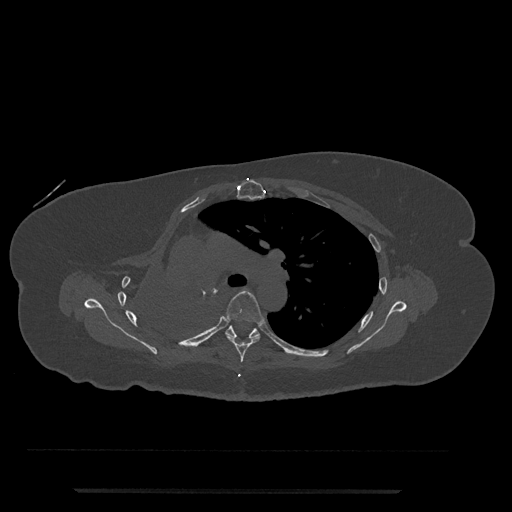
CT including the spine, one axial slice; position 524 of 797 along the scan axis; 120 kVp; bone window (W 1800 / L 400 HU); 0.5 mm slice thickness; 512 × 512 image matrix, field of view 440 × 440 mm. Patient: female, 51 years. Case-level facts recorded for this patient, not image findings: primary cancer: neuro; vertebrae with lytic lesions (as recorded): T8.
Structures marked on this image (semi-automatically segmented with operator editing):
- T5 vertebra: box from (x=206, y=289) to (x=264, y=363) px
- T6 vertebra: (x=225, y=326)–(x=260, y=339)